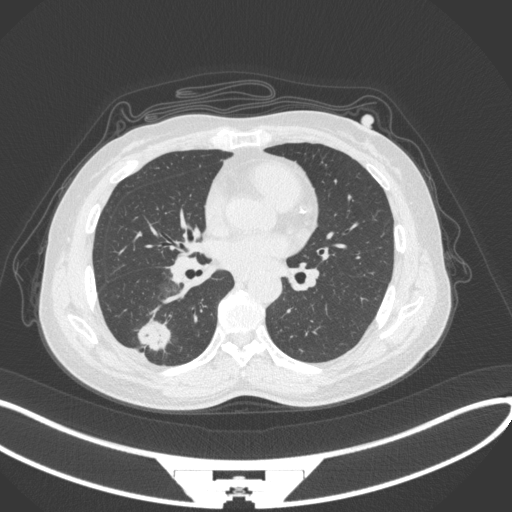
Chest CT, one axial slice; slice 143 of 352 in the series (ordered by position); reconstruction kernel B31f; 120 kVp; lung window (W 1500 / L -600 HU); 512 × 512 image matrix, field of view 400 × 400 mm. Patient: female, 55 years. Case-level facts recorded for this patient, not image findings: clinical TNM (as recorded): T1c N1 M0.
Annotated regions visible in this slice (rectangle marked by the reading radiologist):
- lung tumour (recorded histology: adenocarcinoma): bounding box [x1, y1, x2, y2] px = [133, 315, 176, 352]